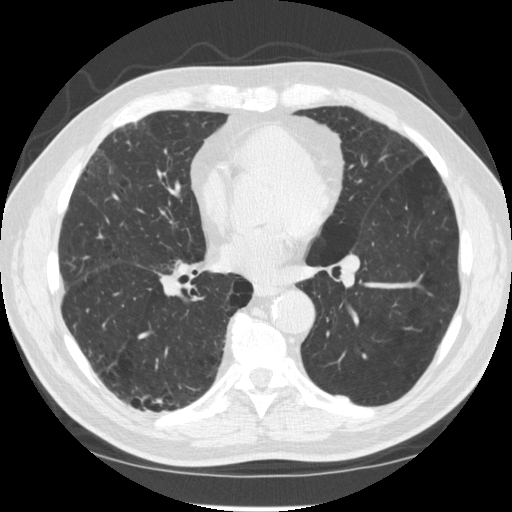
Low-dose screening chest CT, axial slice; second screening round (one year after baseline); lung window (W 1500 / L -600 HU); 512 × 512 image matrix. Male participant, aged 70 years at enrolment. Former smoker at enrolment.
- Expert-annotated lung lesion, bounding box [x1, y1, x2, y2] px = [127, 377, 178, 430].
- The screening reader recorded 2 non-calcified nodules or masses ≥4 mm on this exam; which of them this box marks is not recorded.
- Official screen result: negative screen, significant abnormalities not suspicious for lung cancer.
- Later outcome: lung cancer diagnosed 617 days after this screen (after the third annual screen) — squamous cell carcinoma, NOS, right upper lobe, poorly differentiated (G3), stage IV (AJCC 6th edition).